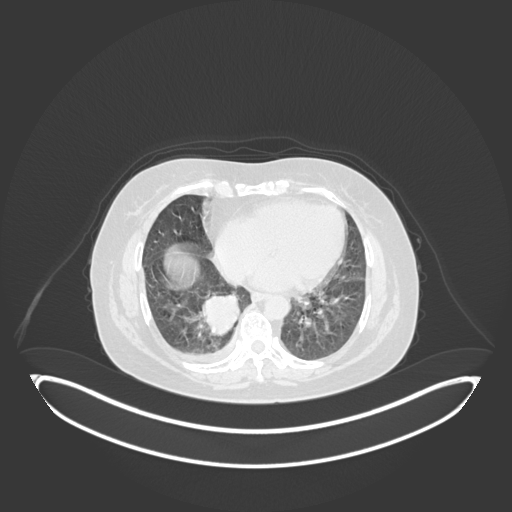
Chest CT, one axial slice. Position 54 of 231 along the scan axis. Reconstruction kernel B30f. 120 kVp. Lung window (W 1500 / L -600 HU). 1 mm slice thickness. 512 × 512 image matrix, field of view 500 × 500 mm. Female patient, age 56 years. From the clinical record (not read from this slice): clinical TNM (as recorded): T2b N1 M0; histopathological grade: G3.
Structures marked on this image (bounding box drawn by a radiologist):
- lung tumour (recorded histology: small cell carcinoma): bounding box [x1, y1, x2, y2] px = [200, 289, 248, 346]